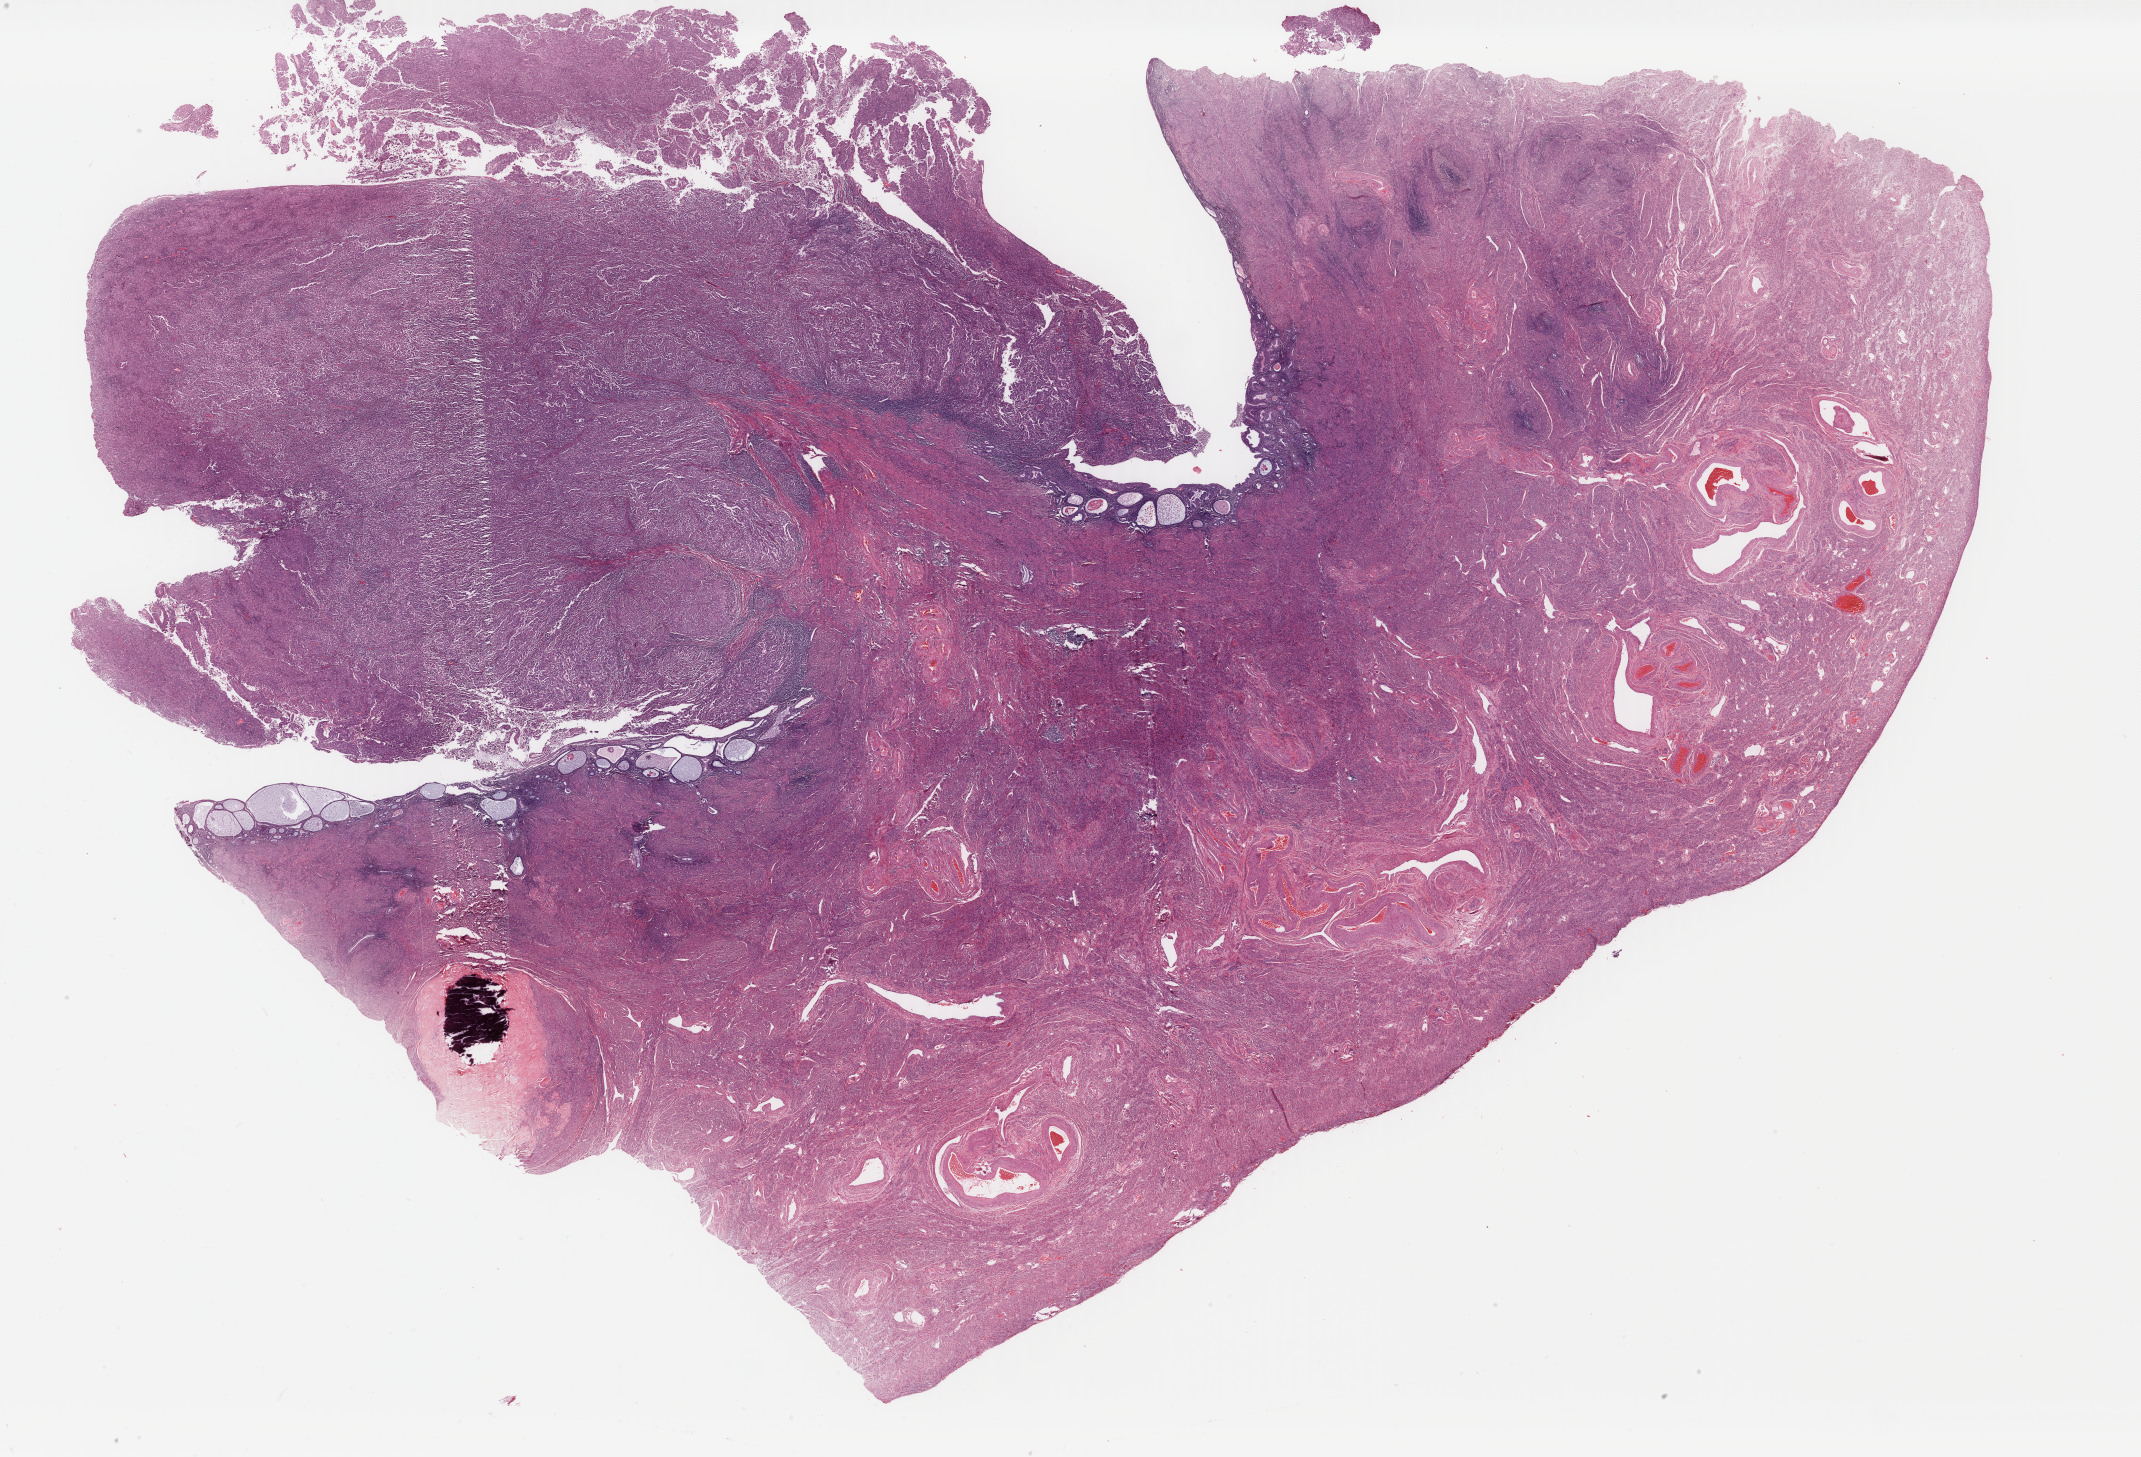
Whole-slide histology image, H&E-stained — shown as a low-resolution overview of the whole scanned area (about 34.0 x 23.1 mm, acquisition: 40x scan). Formalin-fixed paraffin-embedded (FFPE) diagnostic section. Primary tumour sample from the uterus. Female patient; age at initial diagnosis 67 years. Histologic grade: G3 (poorly differentiated).
Pathologic diagnosis: Serous cystadenocarcinoma, NOS (endometrium). FIGO stage: IA.